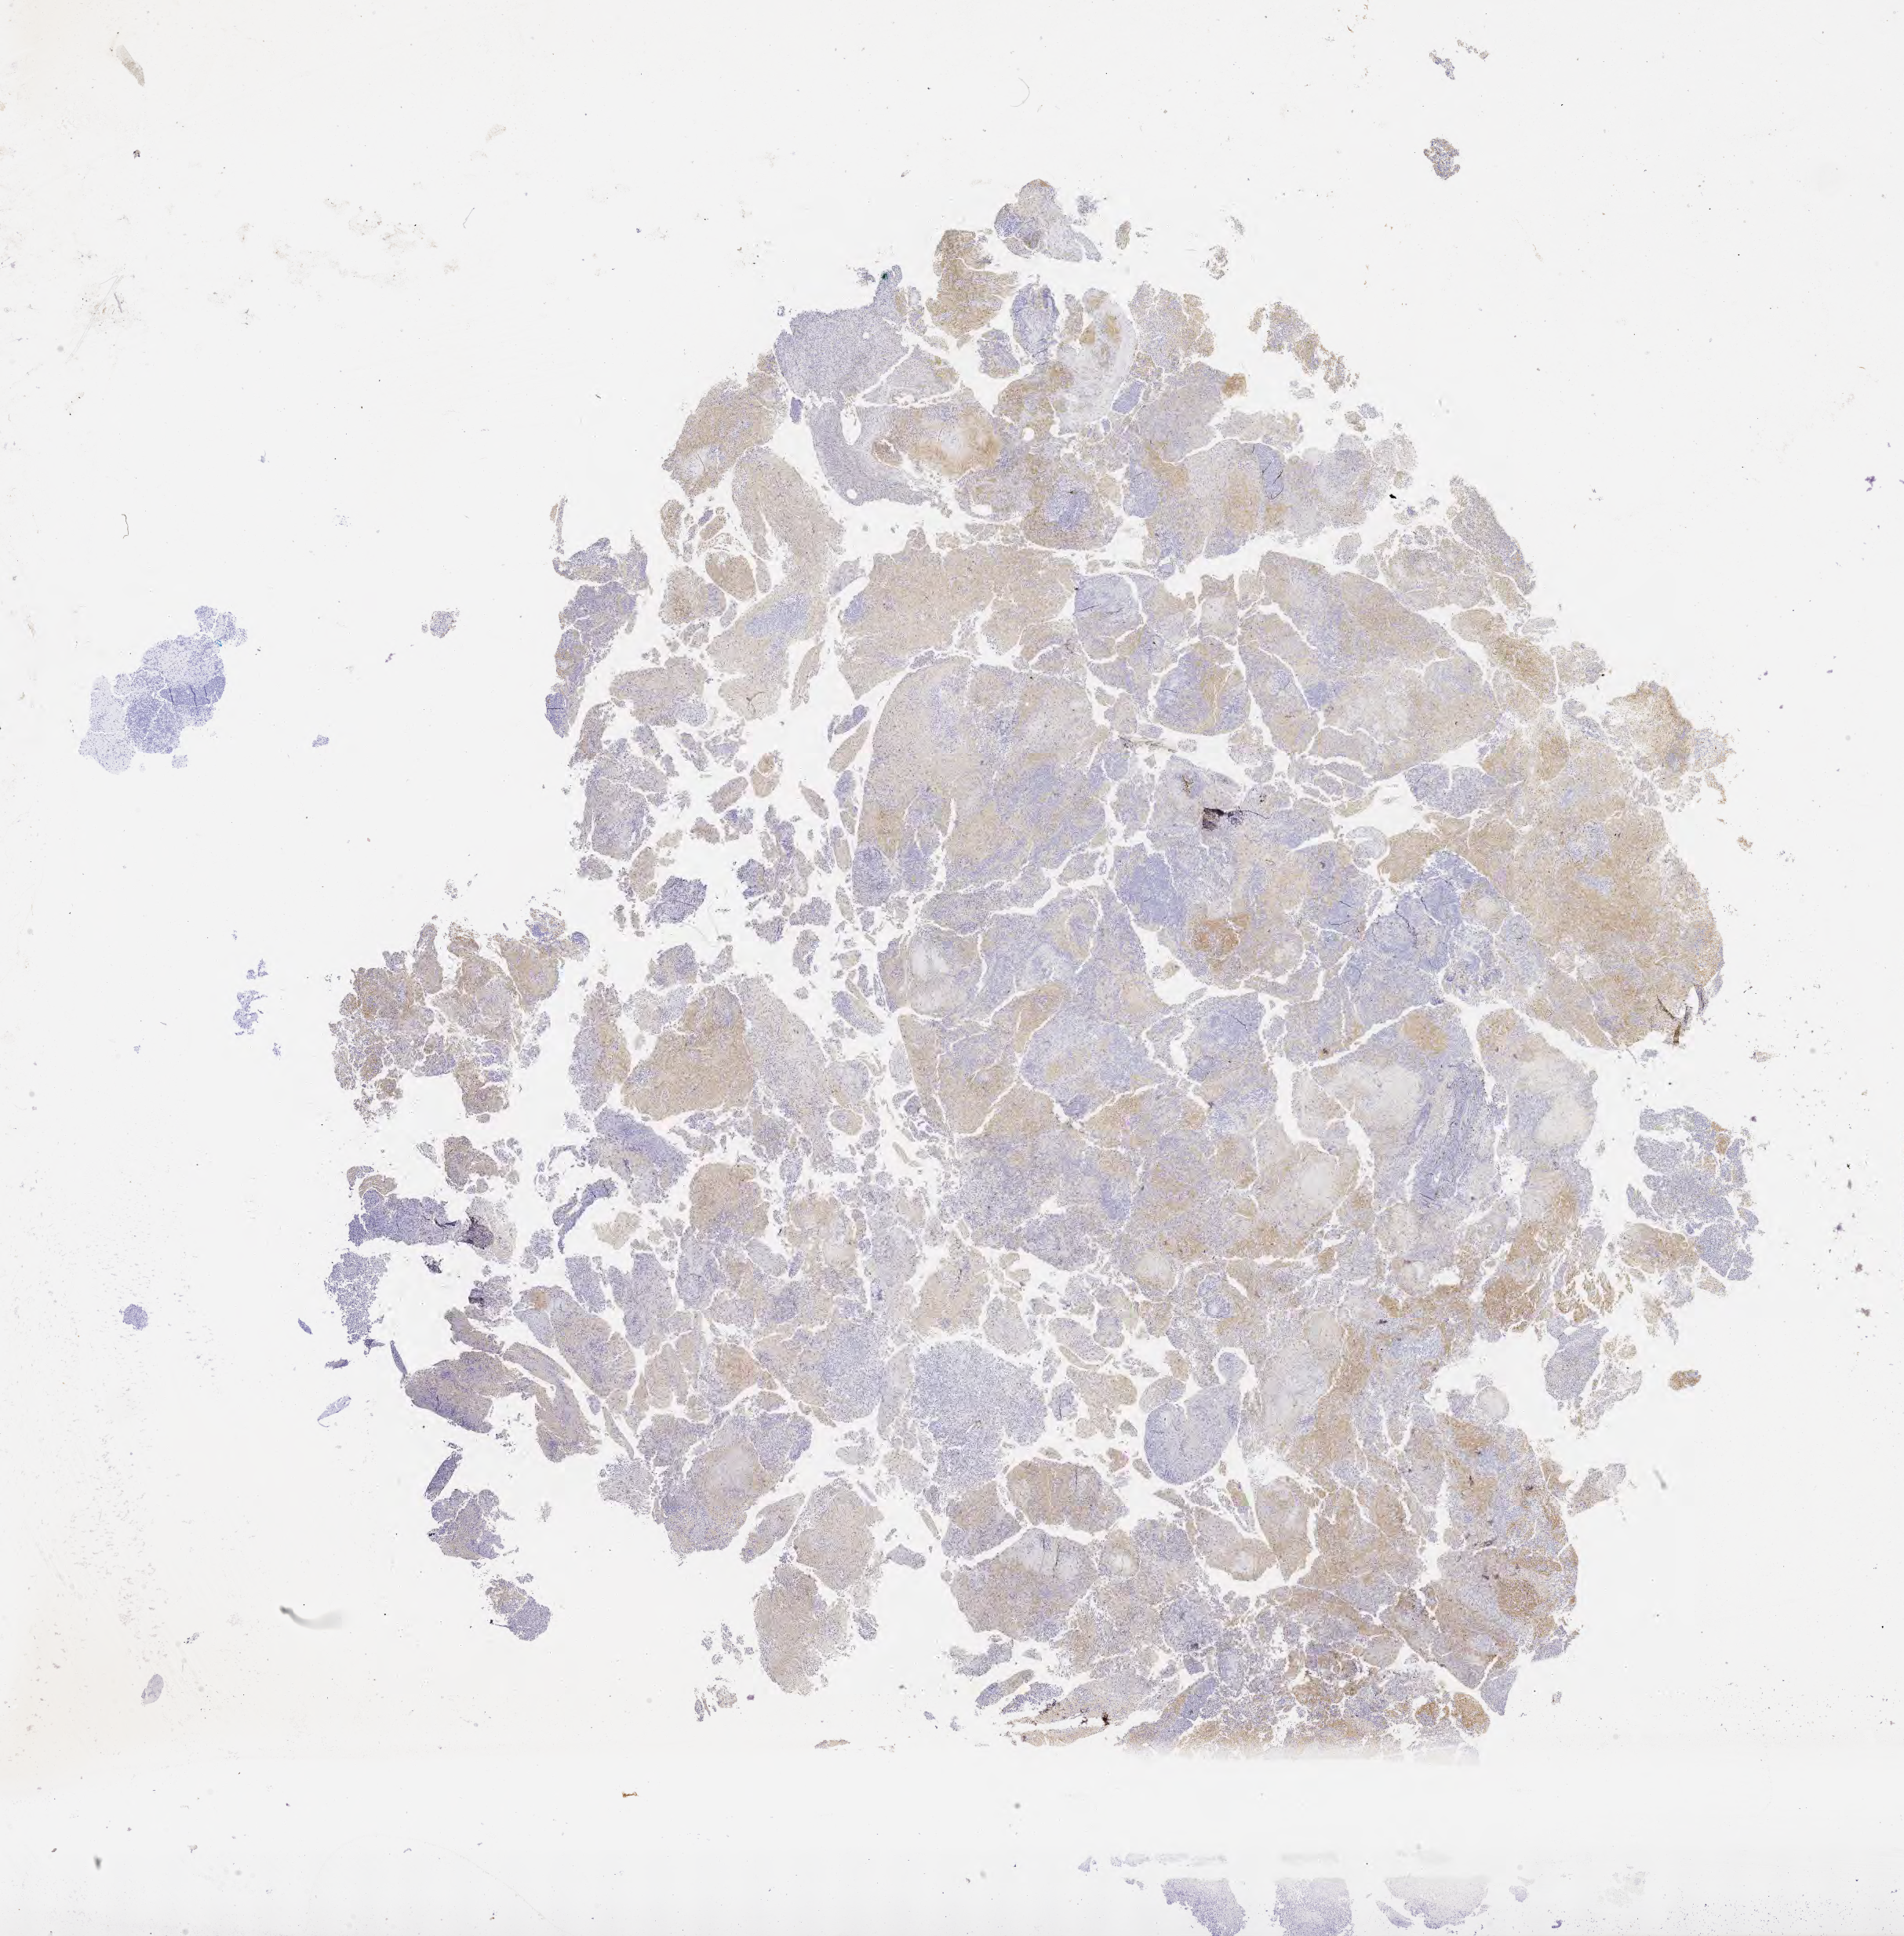
Whole-slide image, immunohistochemical stain for CD10, low-resolution overview of the scanned area, about 19.6 x 20.0 mm, tumor tissue, anatomic site: brain. Patient male; aged 51.
Diagnosis: Diffuse large B-cell lymphoma, NOS.